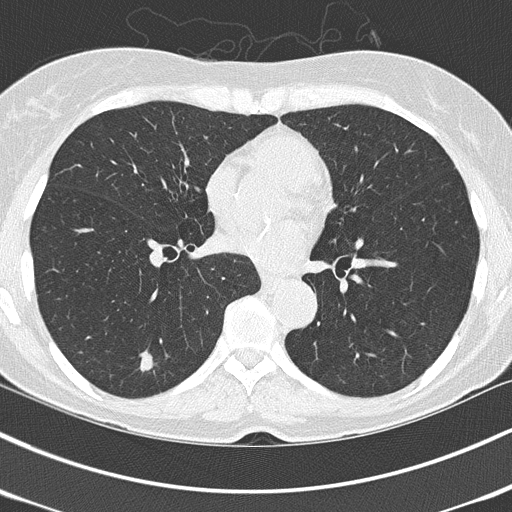
Low-dose screening chest CT, axial slice. Third annual screen. Lung window (W 1500 / L -600 HU). 2 mm slice thickness. 120 kVp. Slice 86 of 150 in the series. Female participant, aged 67 years at enrolment. Current smoker at enrolment.
• Expert reader's lesion annotation, bounding box <128,348,167,384> (left, top, right, bottom; pixels).
• The screening reader recorded 3 non-calcified nodules or masses ≥4 mm on this exam (right lower lobe, right lower lobe, left lower lobe); which of them this box marks is not recorded.
• Official screen result: positive, other.
• Participant outcome: lung cancer diagnosed 64 days after this screen — adenocarcinoma, NOS, left lower lobe, poorly differentiated (G3), stage IA (AJCC 6th edition), 25 mm at pathology.